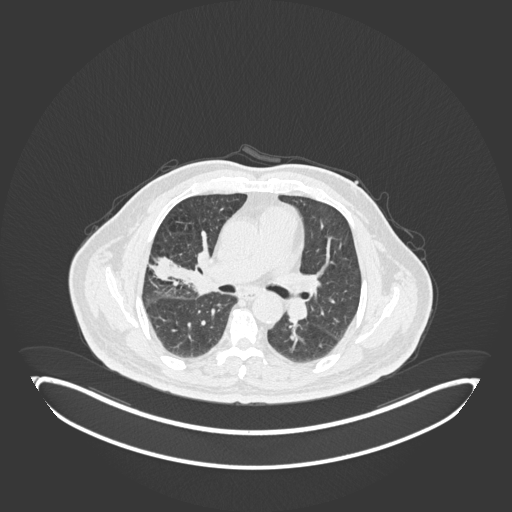
Chest CT, one axial slice. Lung window (W 1500 / L -600 HU). 1 mm slice thickness. 512 × 512 image matrix, field of view 500 × 500 mm. Male patient, age 72 years. From the clinical record (not read from this slice): clinical TNM (as recorded): T1c N0 M0.
Outlined on this slice (rectangle marked by the reading radiologist):
- lung tumour (recorded histology: squamous cell carcinoma): bounding box <179,246,215,296> (left, top, right, bottom; pixels)